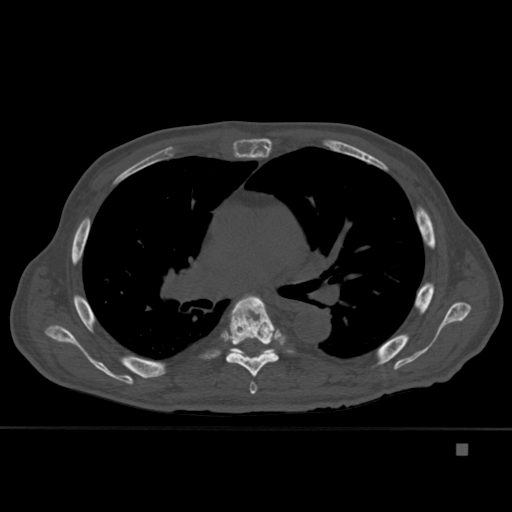
CT including the spine, one axial slice. Position 293 of 451 along the scan axis. Bone window (W 1800 / L 400 HU). 1.5 mm slice thickness. 512 × 512 image matrix, field of view 378 × 378 mm. Patient: male, 75 years. Case-level facts recorded for this patient, not image findings: primary cancer: prostate.
Annotated regions visible in this slice (semi-automatically segmented with operator editing):
- T5 vertebra: bounding box <249,381,257,394> (left, top, right, bottom; pixels)
- T6 vertebra: <223,295,279,377>
- T7 vertebra: <231,348,274,356>